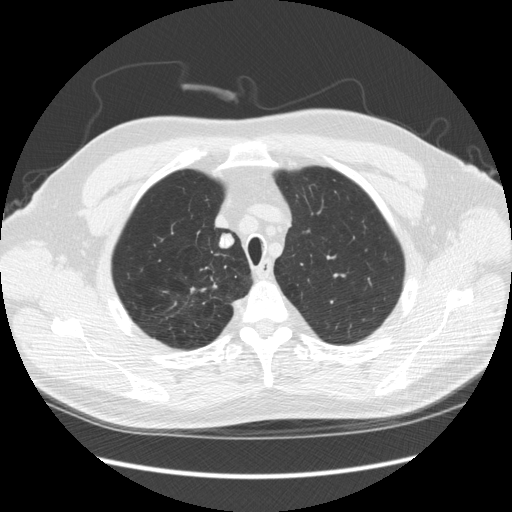
Chest CT (low-dose screening protocol), one axial image. Third screening round (two years after baseline). Lung window (W 1500 / L -600 HU). Slice 38 of 248 in the series. Male participant, aged 64 years at enrolment. Former smoker at enrolment.
Lesion marked by an expert reader, bounding box <200,230,242,260> (left, top, right, bottom; pixels). The screening reader recorded 4 non-calcified nodules or masses ≥4 mm on this exam (right upper lobe, right upper lobe, right upper lobe, right upper lobe); which of them this box marks is not recorded.